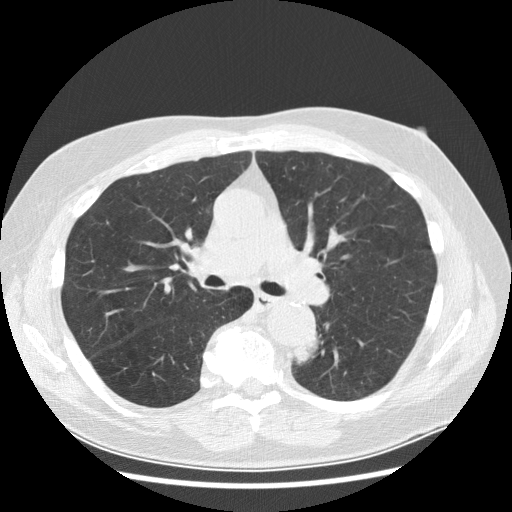
Low-dose screening chest CT, axial slice. Baseline annual screen. Lung window (W 1500 / L -600 HU). Standard (soft-tissue) reconstruction kernel (STANDARD). Slice 110 of 282 in the series. Male, age 70 years at enrolment. Current smoker at enrolment.
Expert-annotated lung lesion, box from (x=279, y=325) to (x=332, y=384) px. Reader record for this screening exam (exam-level; its link to the box is not recorded): non-calcified nodule or mass ≥4 mm, left lower lobe, 27 × 16 mm, spiculated (stellate) margins, soft tissue attenuation, pre-existing on the prior screen: yes; interval growth: yes. Lung cancer was diagnosed 97 days after this screen: papillary adenocarcinoma, NOS, left lower lobe, moderately differentiated (G2), stage IB (AJCC 6th edition), 35 mm at pathology.